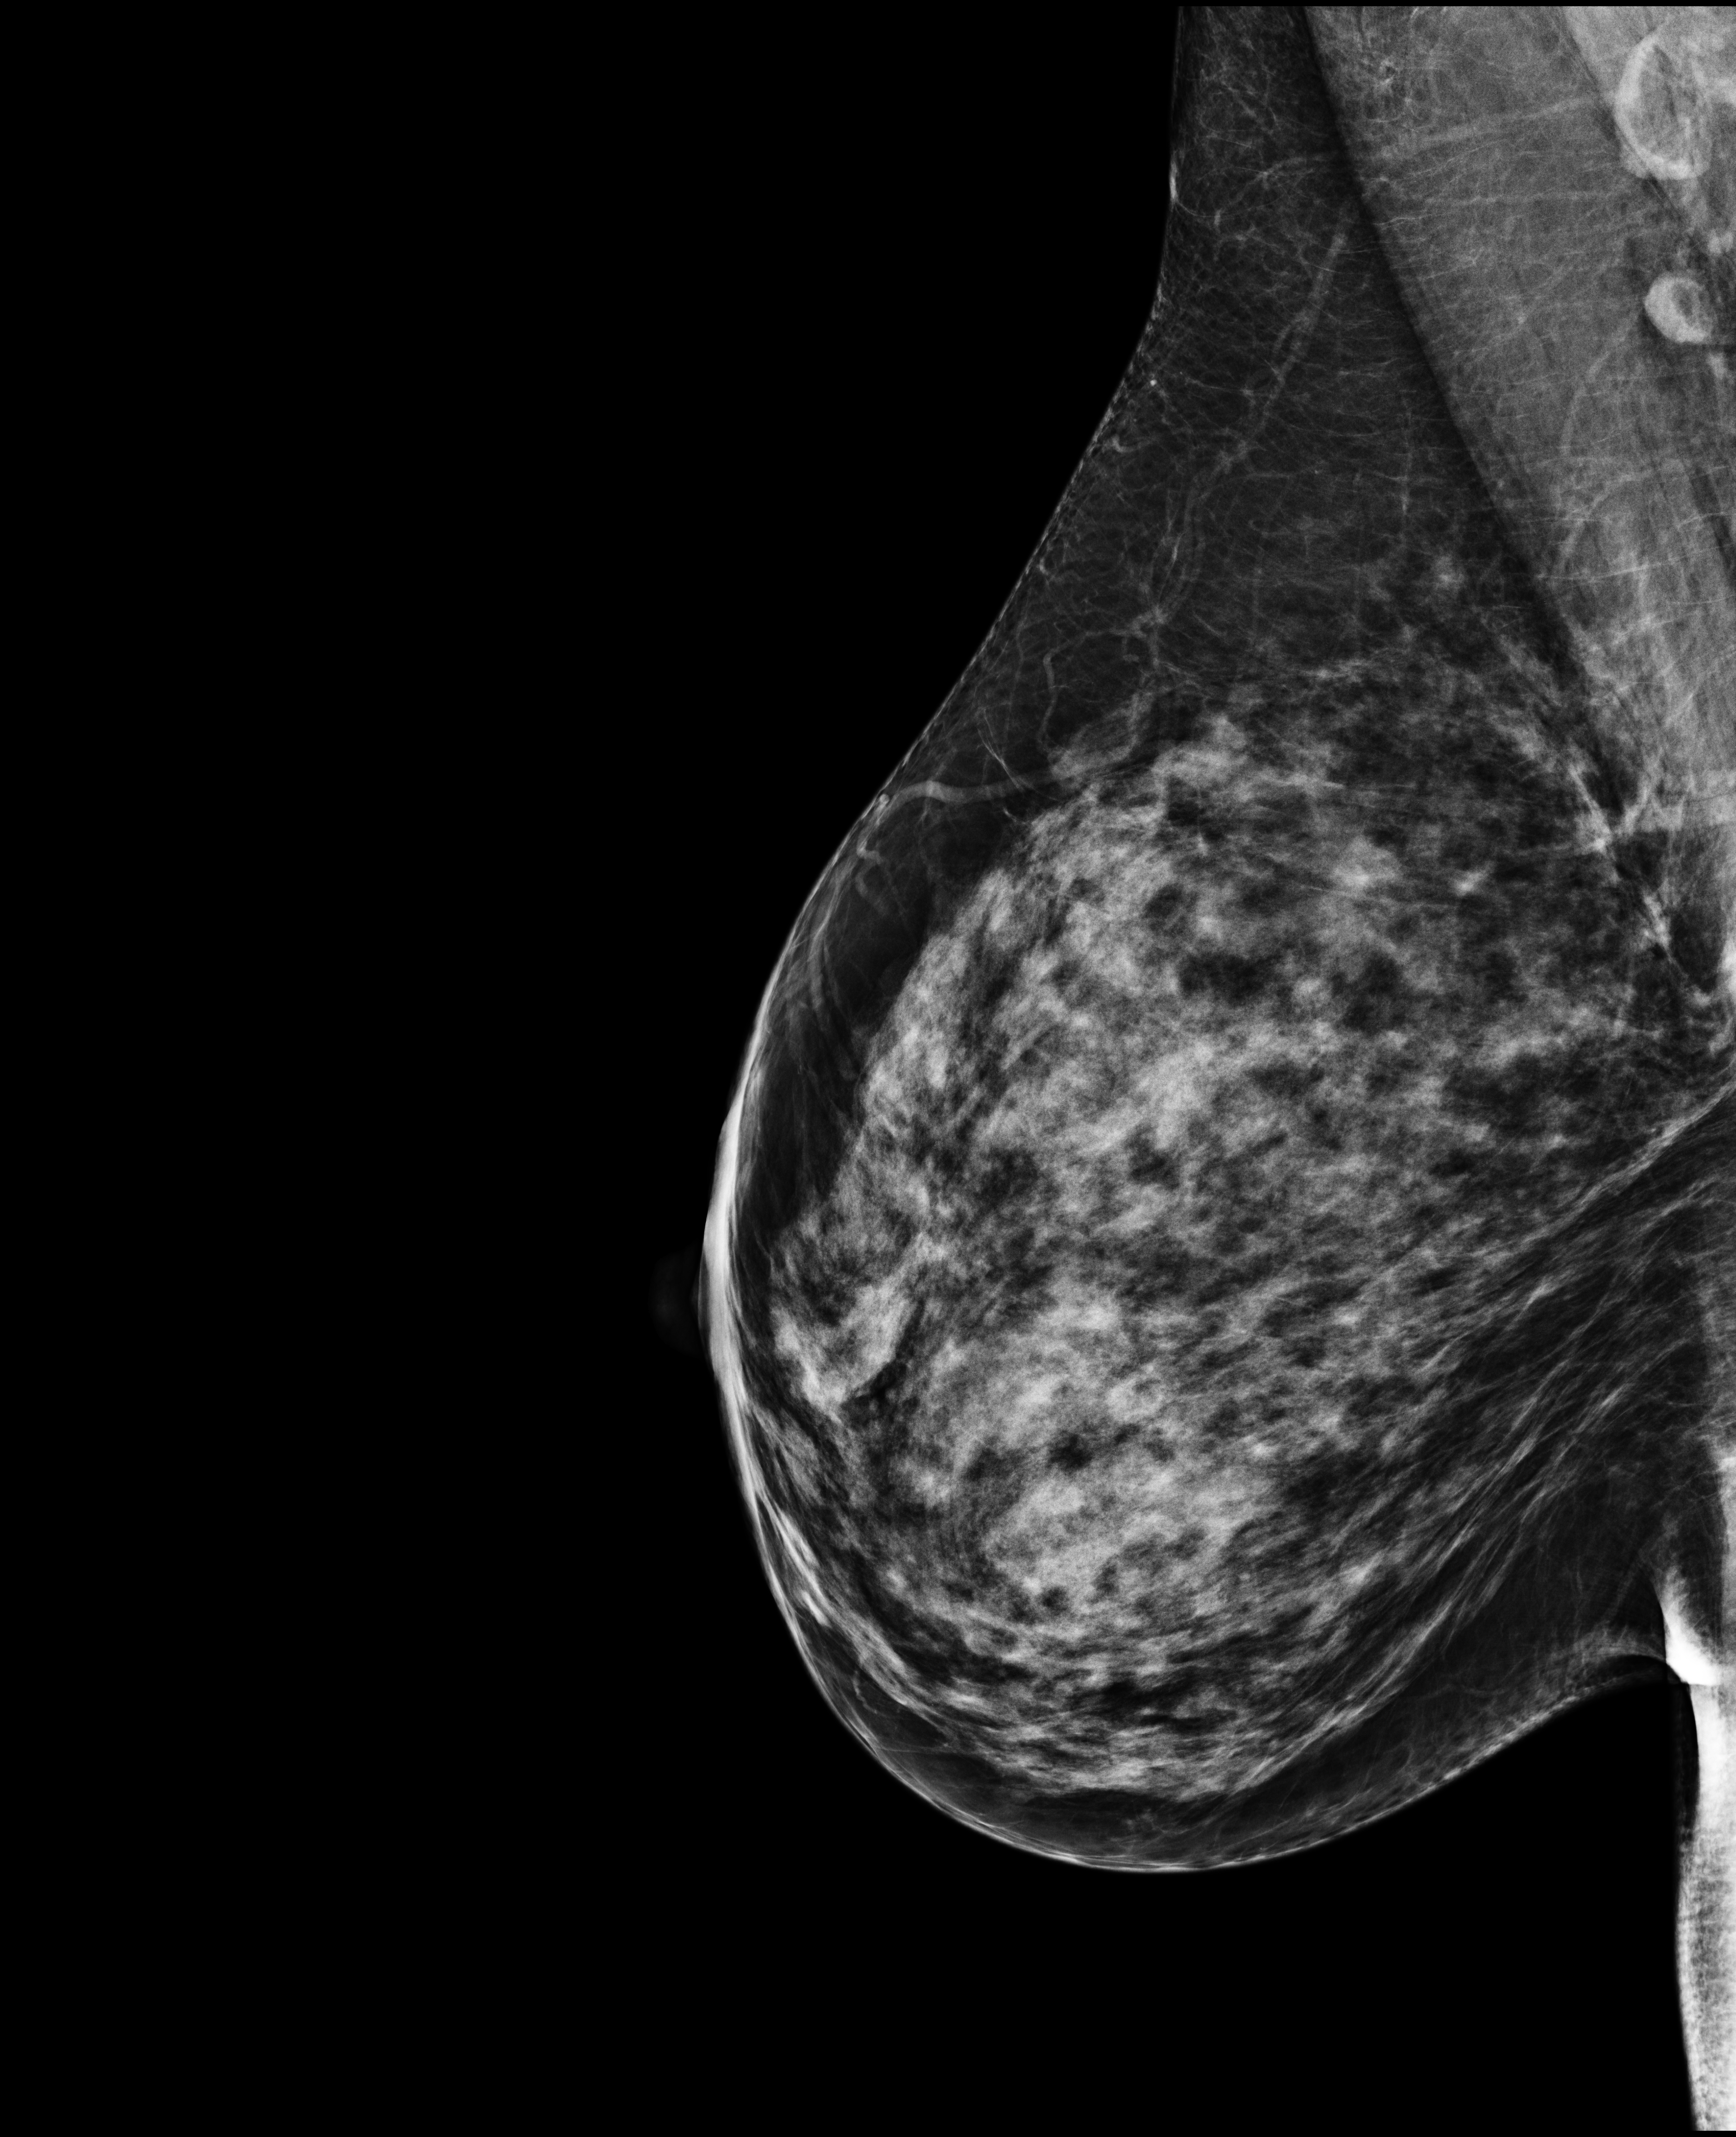
Annual screening mammography examination; compressed breast thickness 68 mm; system: Selenia Dimensions. Female patient, age 45 years.
Image type: full-field digital mammogram. Breast: right. Projection: MLO view.